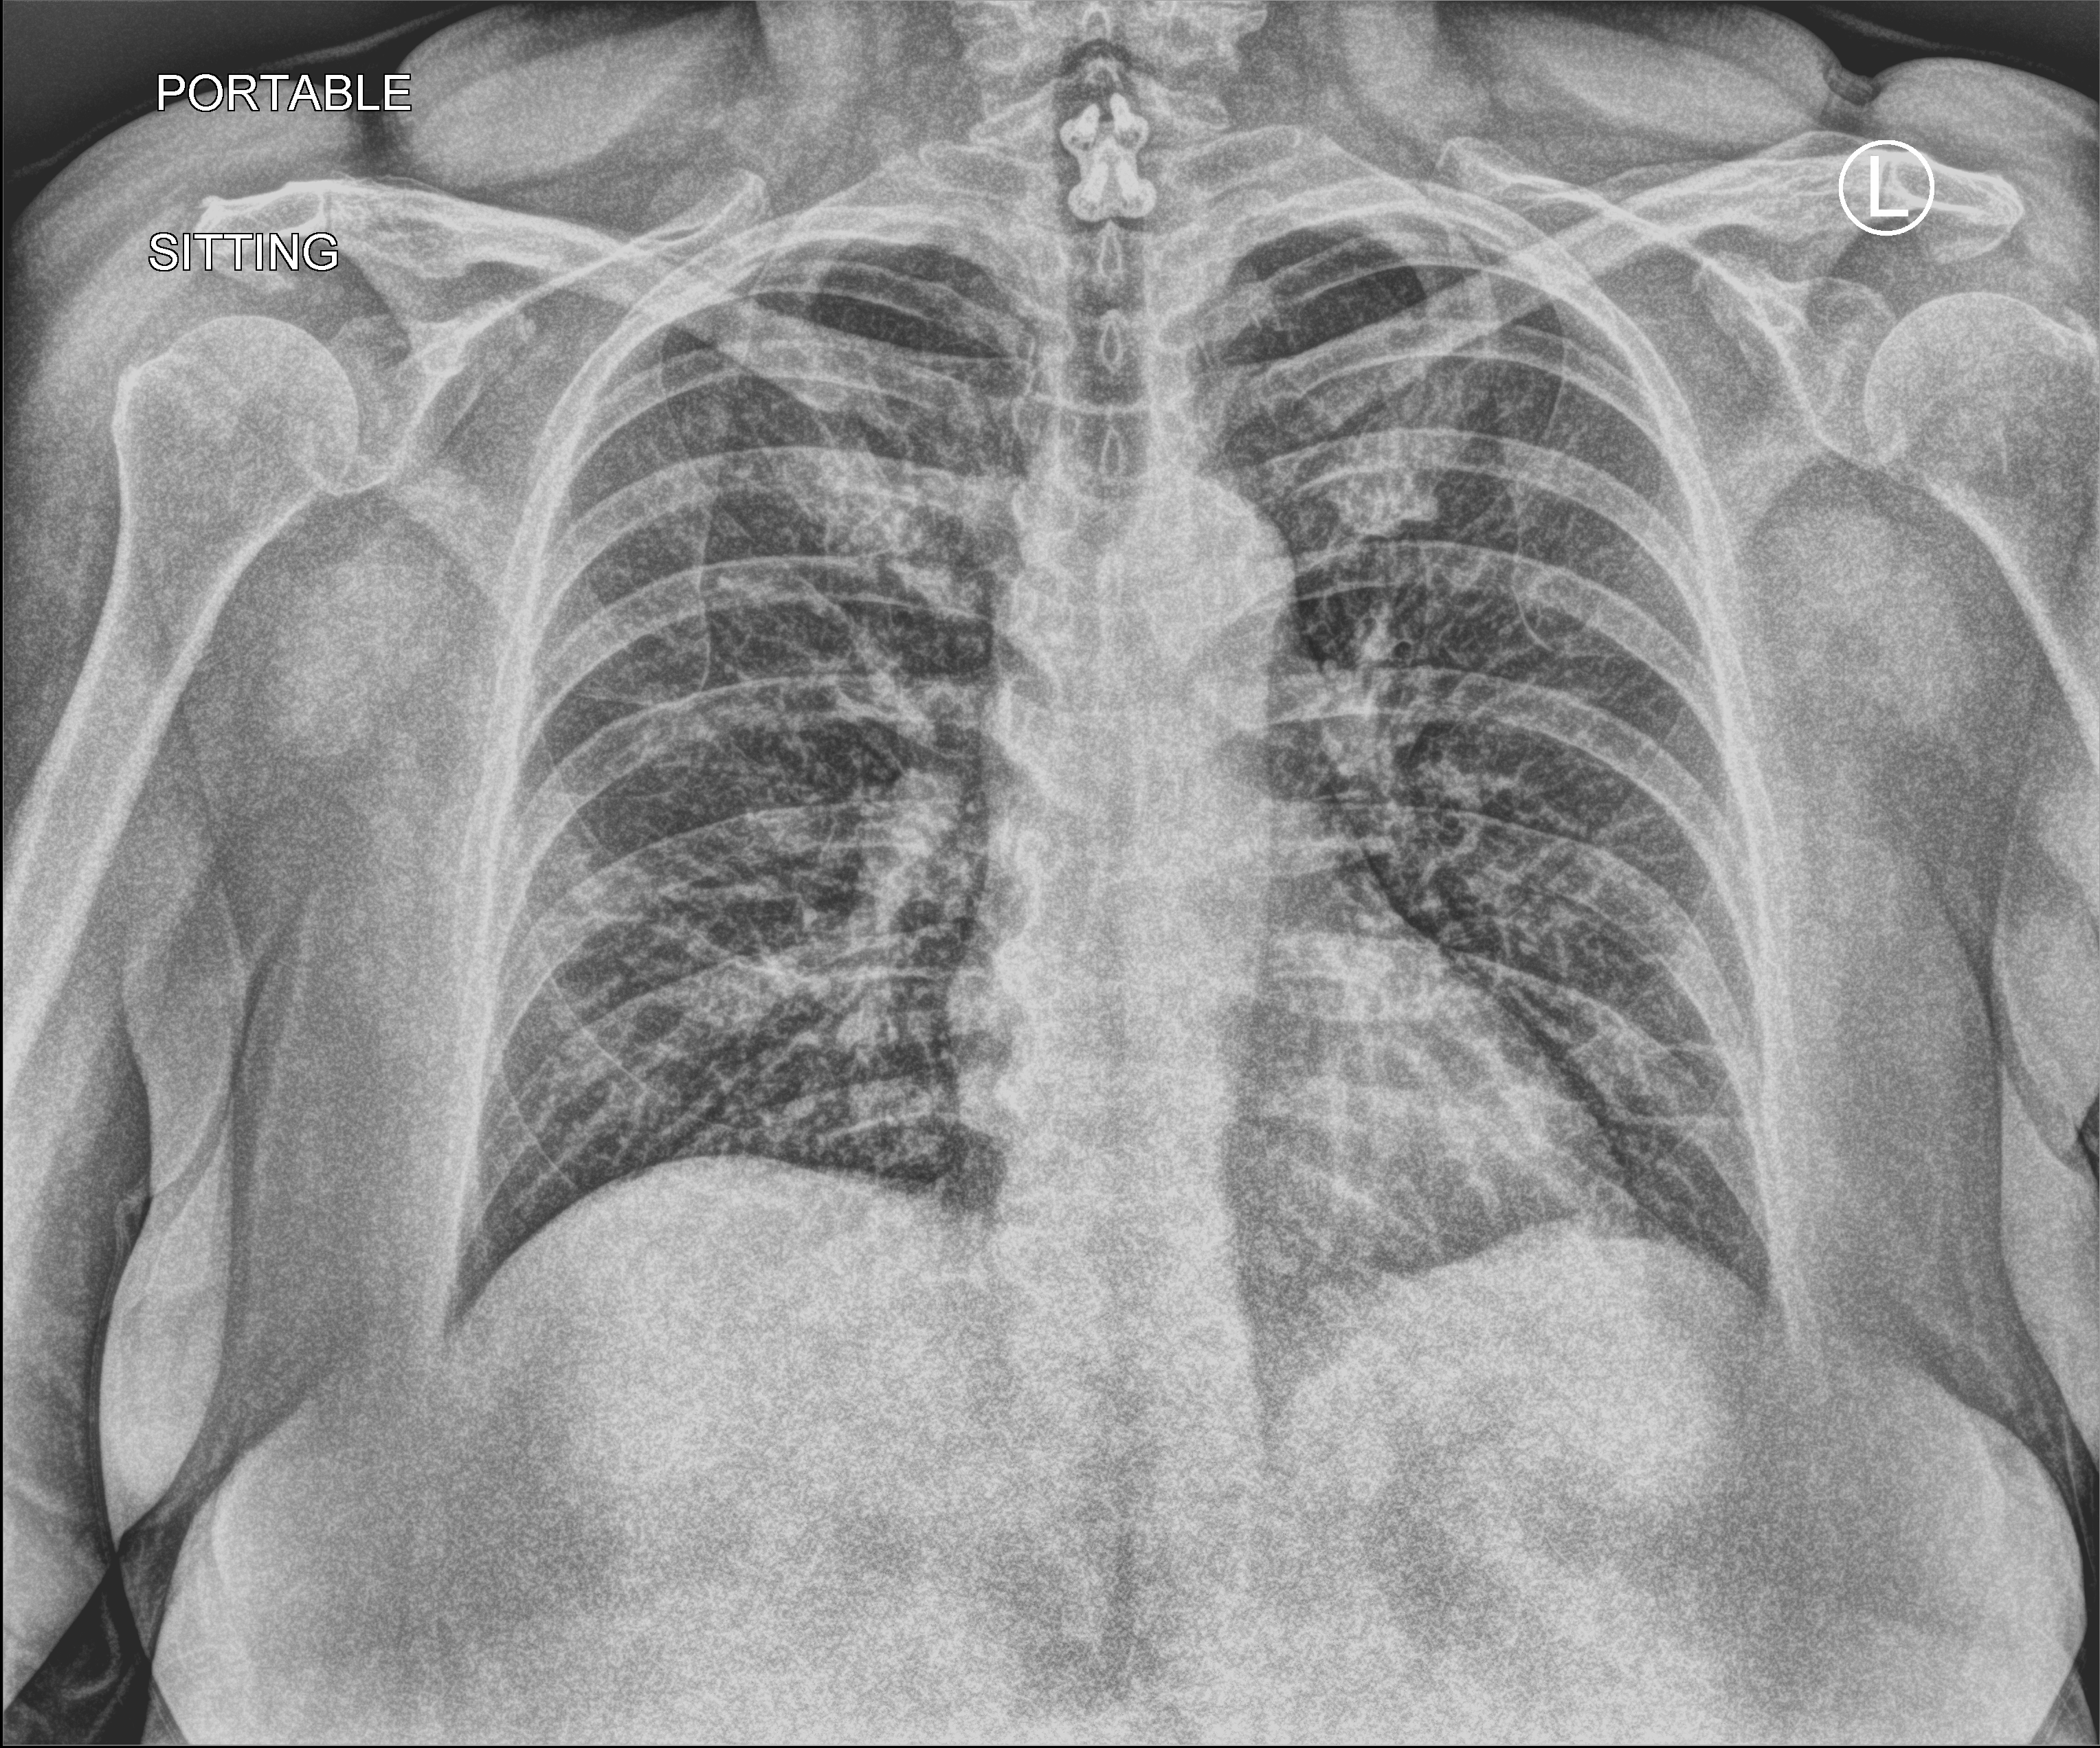
Bedside chest radiograph (computed radiography), anteroposterior (AP) projection. Patient hospitalised with COVID-19; female, aged 18–59 years.
From the hospital-stay record, not from the radiograph (when in the stay this image was taken is not recorded):
- length of hospital stay: 1 day